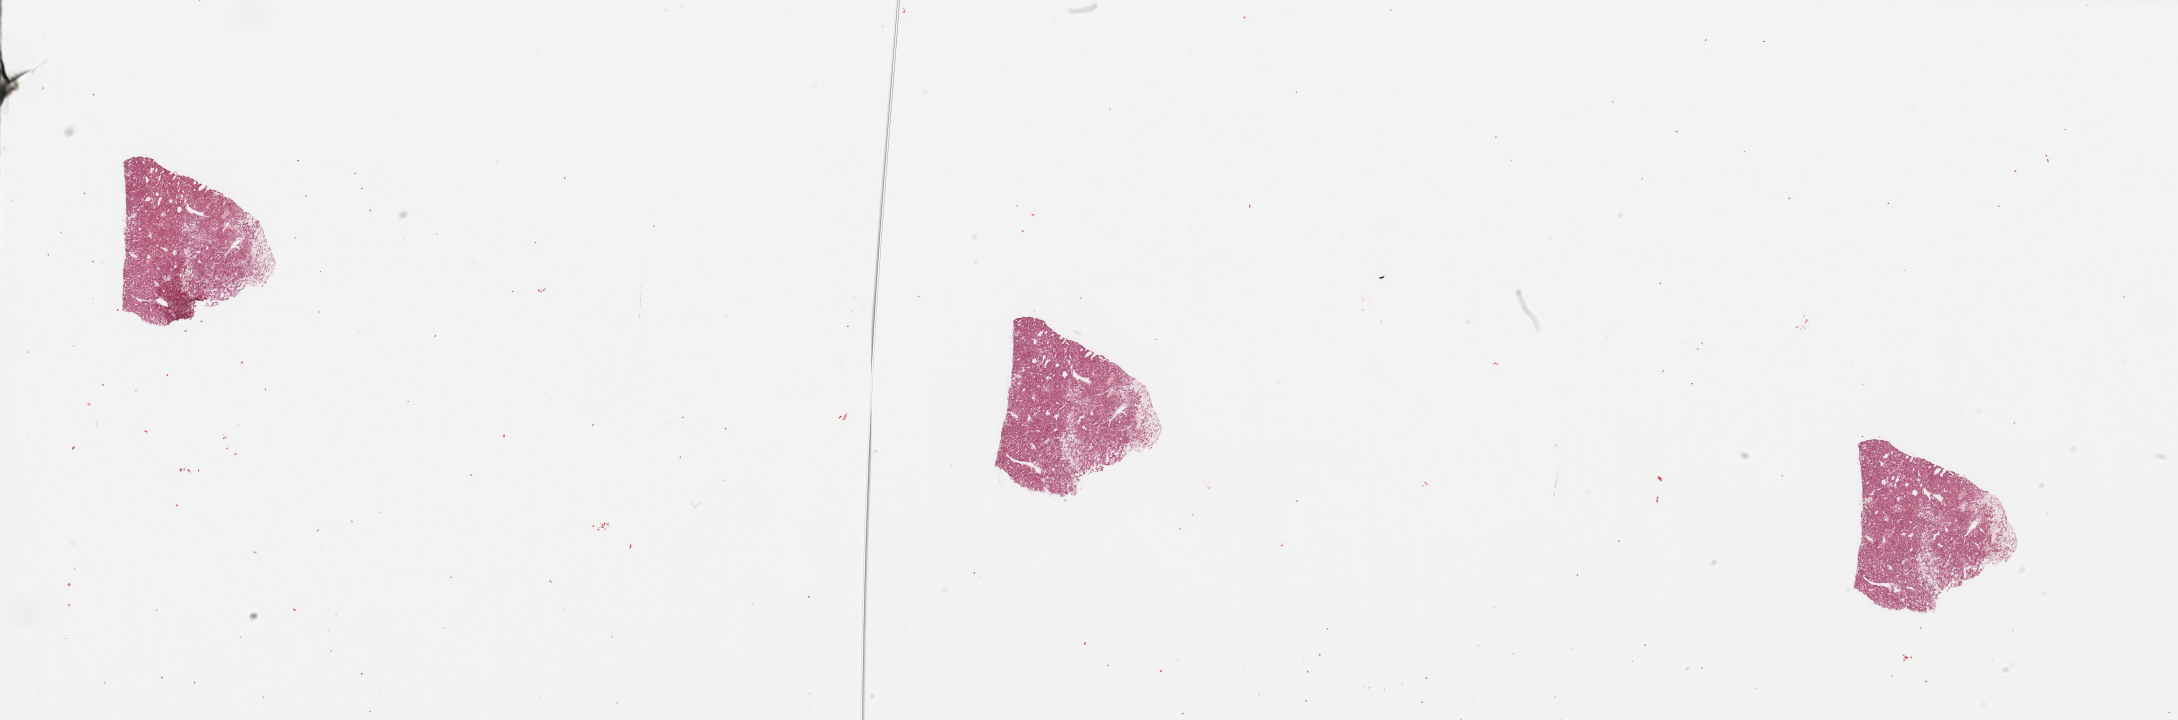
H&E whole-slide image — shown as a low-resolution overview of the whole scanned area (about 34.5 x 11.4 mm, slide scanned at 20x), tumour tissue sample, sampled site: kidney. 63-year-old male patient. Histologic grade: G2 (moderately differentiated). Slide review estimates, as recorded: tumour nuclei 85%, necrosis 0%.
AJCC pathologic stage: III. Histologic diagnosis: Renal cell carcinoma, NOS. Primary tumour site (as recorded): upper pole.